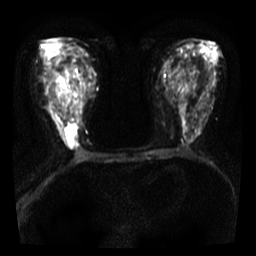
Breast MRI, one axial slice; position 18 of 36 along the scan axis; diffusion-weighted series; image 2 of 4 stored at this slice position (different b-values; order by instance number); 3 T; 5 mm slice thickness; 256 × 256 image matrix, field of view 300 × 300 mm. Female patient.
Outlined on this slice (manually delineated by an expert):
- tumour on diffusion-weighted imaging: bounding box (x1, y1, x2, y2) in pixels: (64, 122, 76, 138)